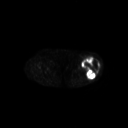
FDG PET of an extremity soft-tissue mass (from a PET/CT study), one axial slice; 3.27 mm slice thickness; 128 × 128 image matrix, field of view 700 × 700 mm. Female patient, age 62 years. Case-level facts recorded for this patient, not image findings: histological type: undifferentiated – high grade; grade: high; site of the primary tumour: left thigh.
Annotated regions visible in this slice (expert contour drawn on MRI and transferred to this co-registered scan by the dataset authors):
- gross tumour volume including surrounding oedema: box from (x=81, y=56) to (x=100, y=79) px
- gross tumour volume (mass): (x=81, y=56)–(x=100, y=79)